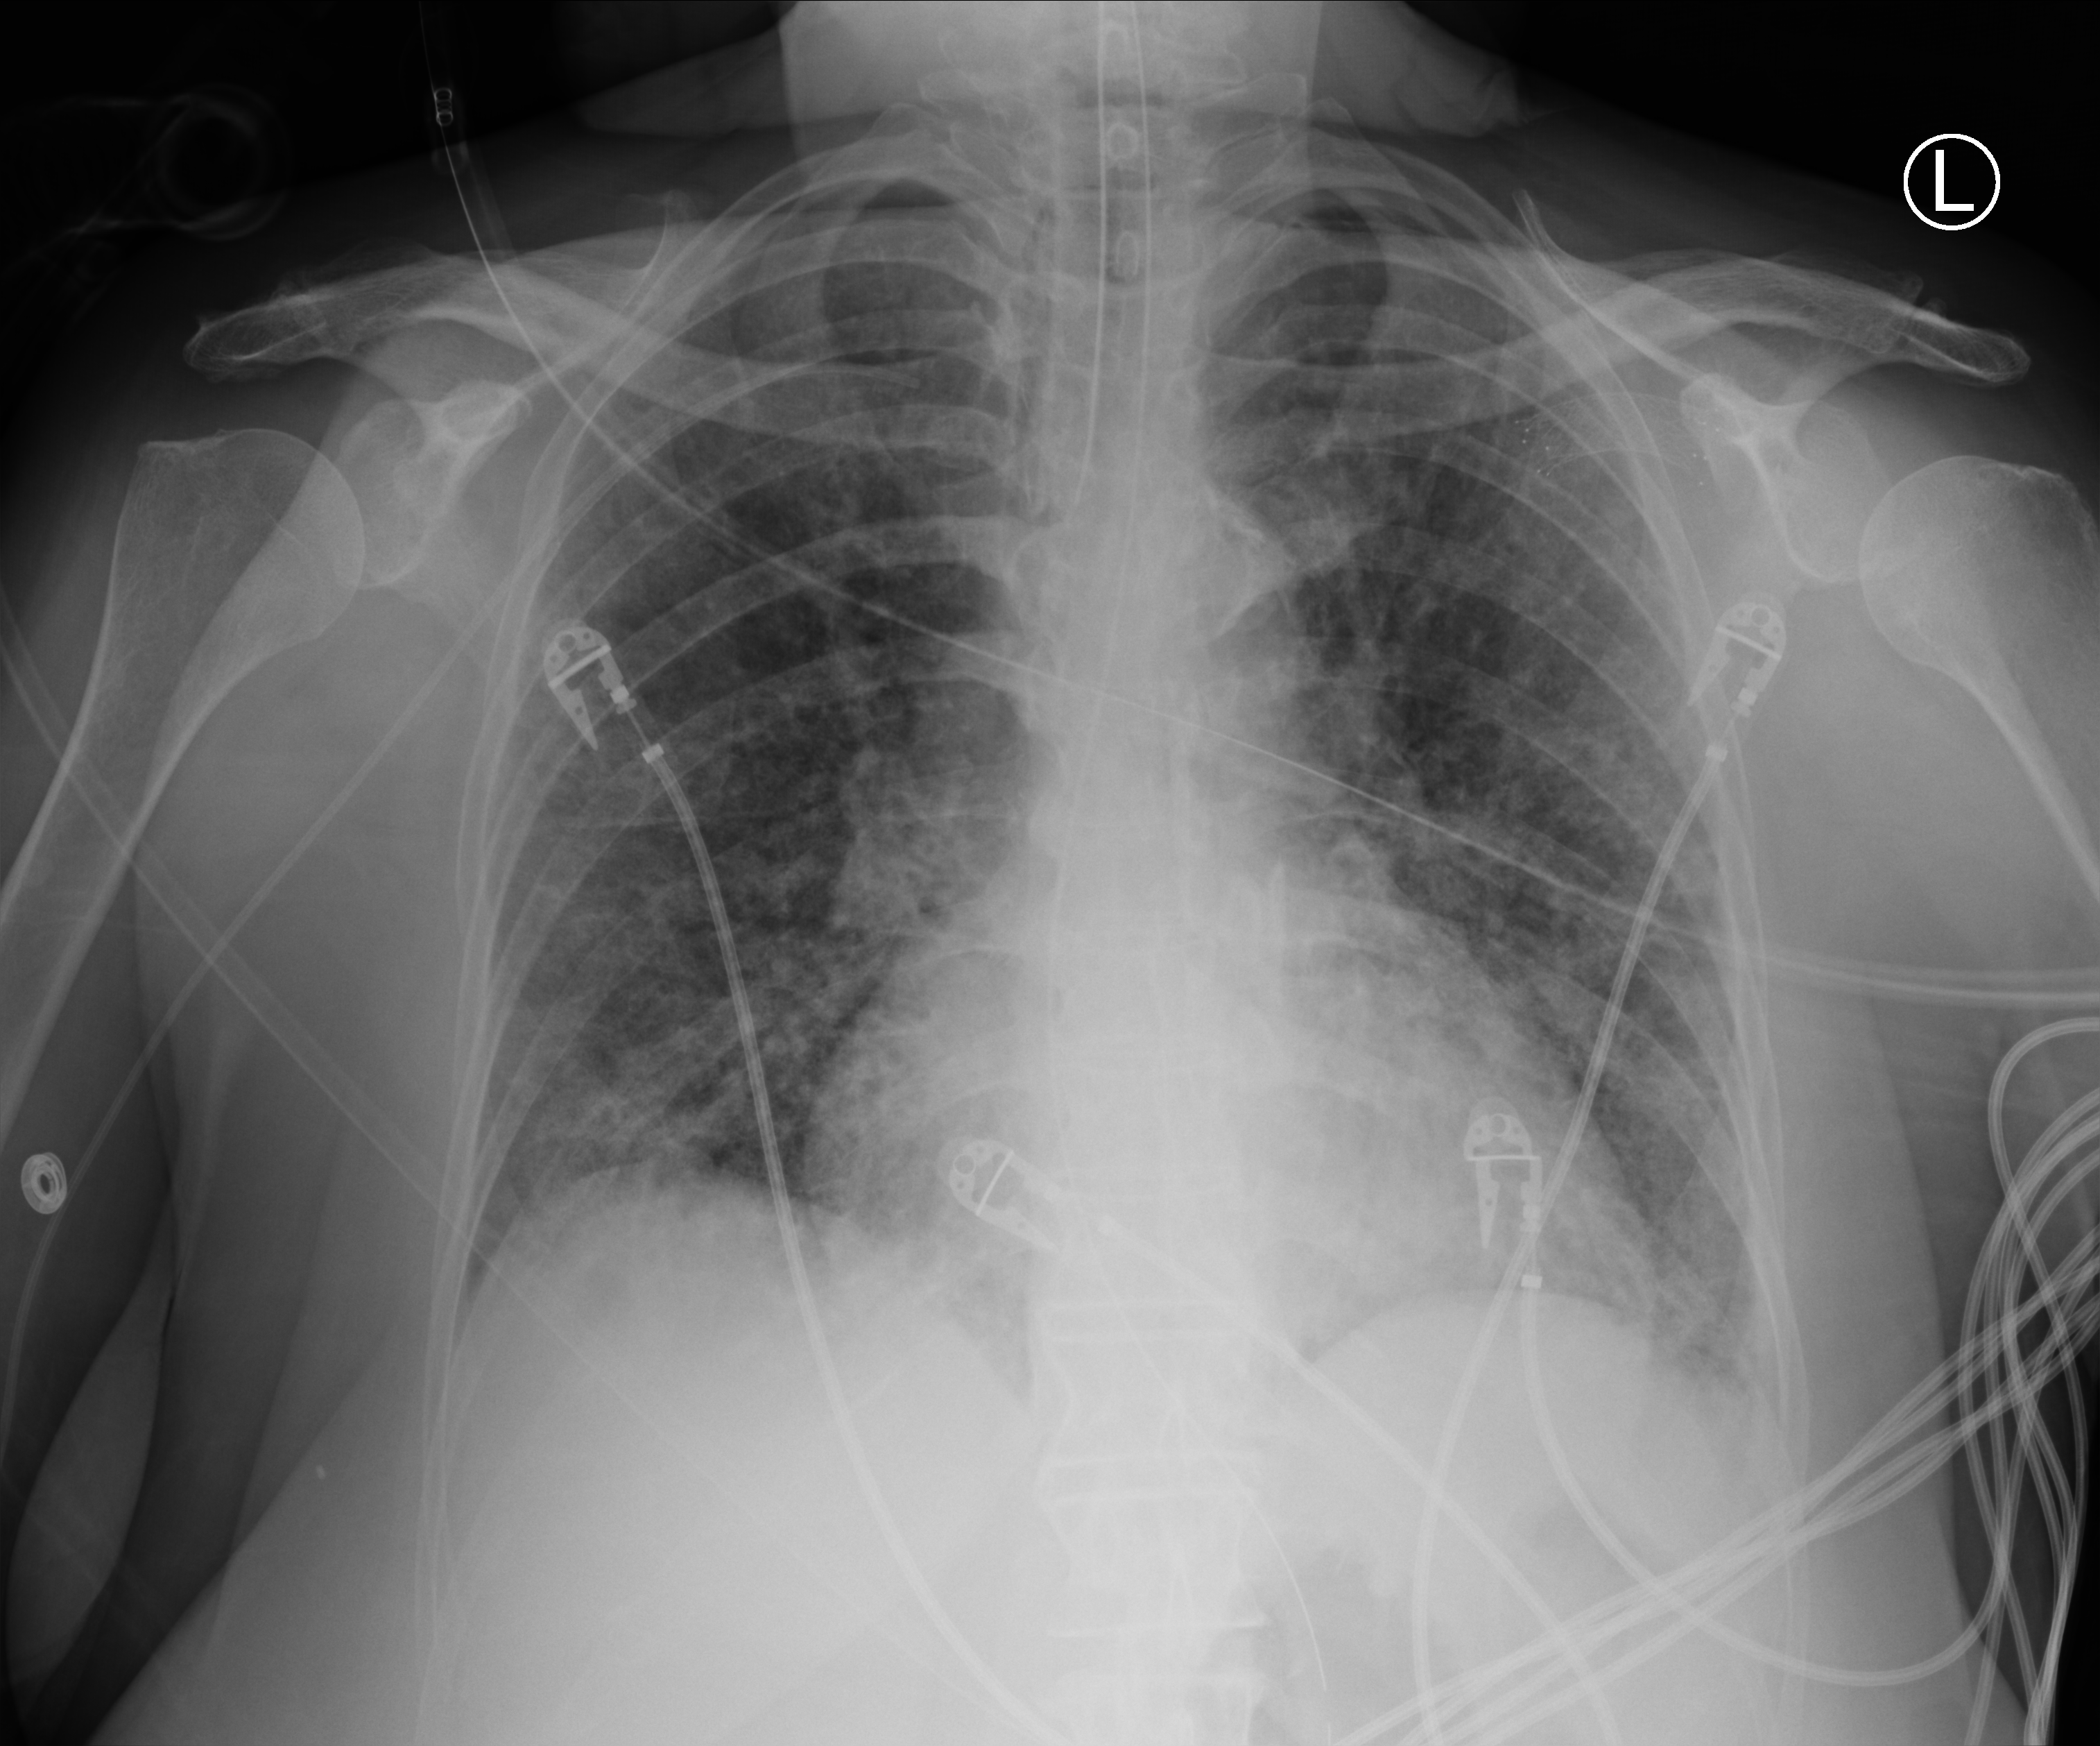
Portable chest radiograph, anteroposterior (AP) projection. Female patient hospitalised with COVID-19, age 60–74 years.
Admission-level facts for this patient (not findings on this image; timing relative to this image not recorded):
- length of hospital stay: 23 days